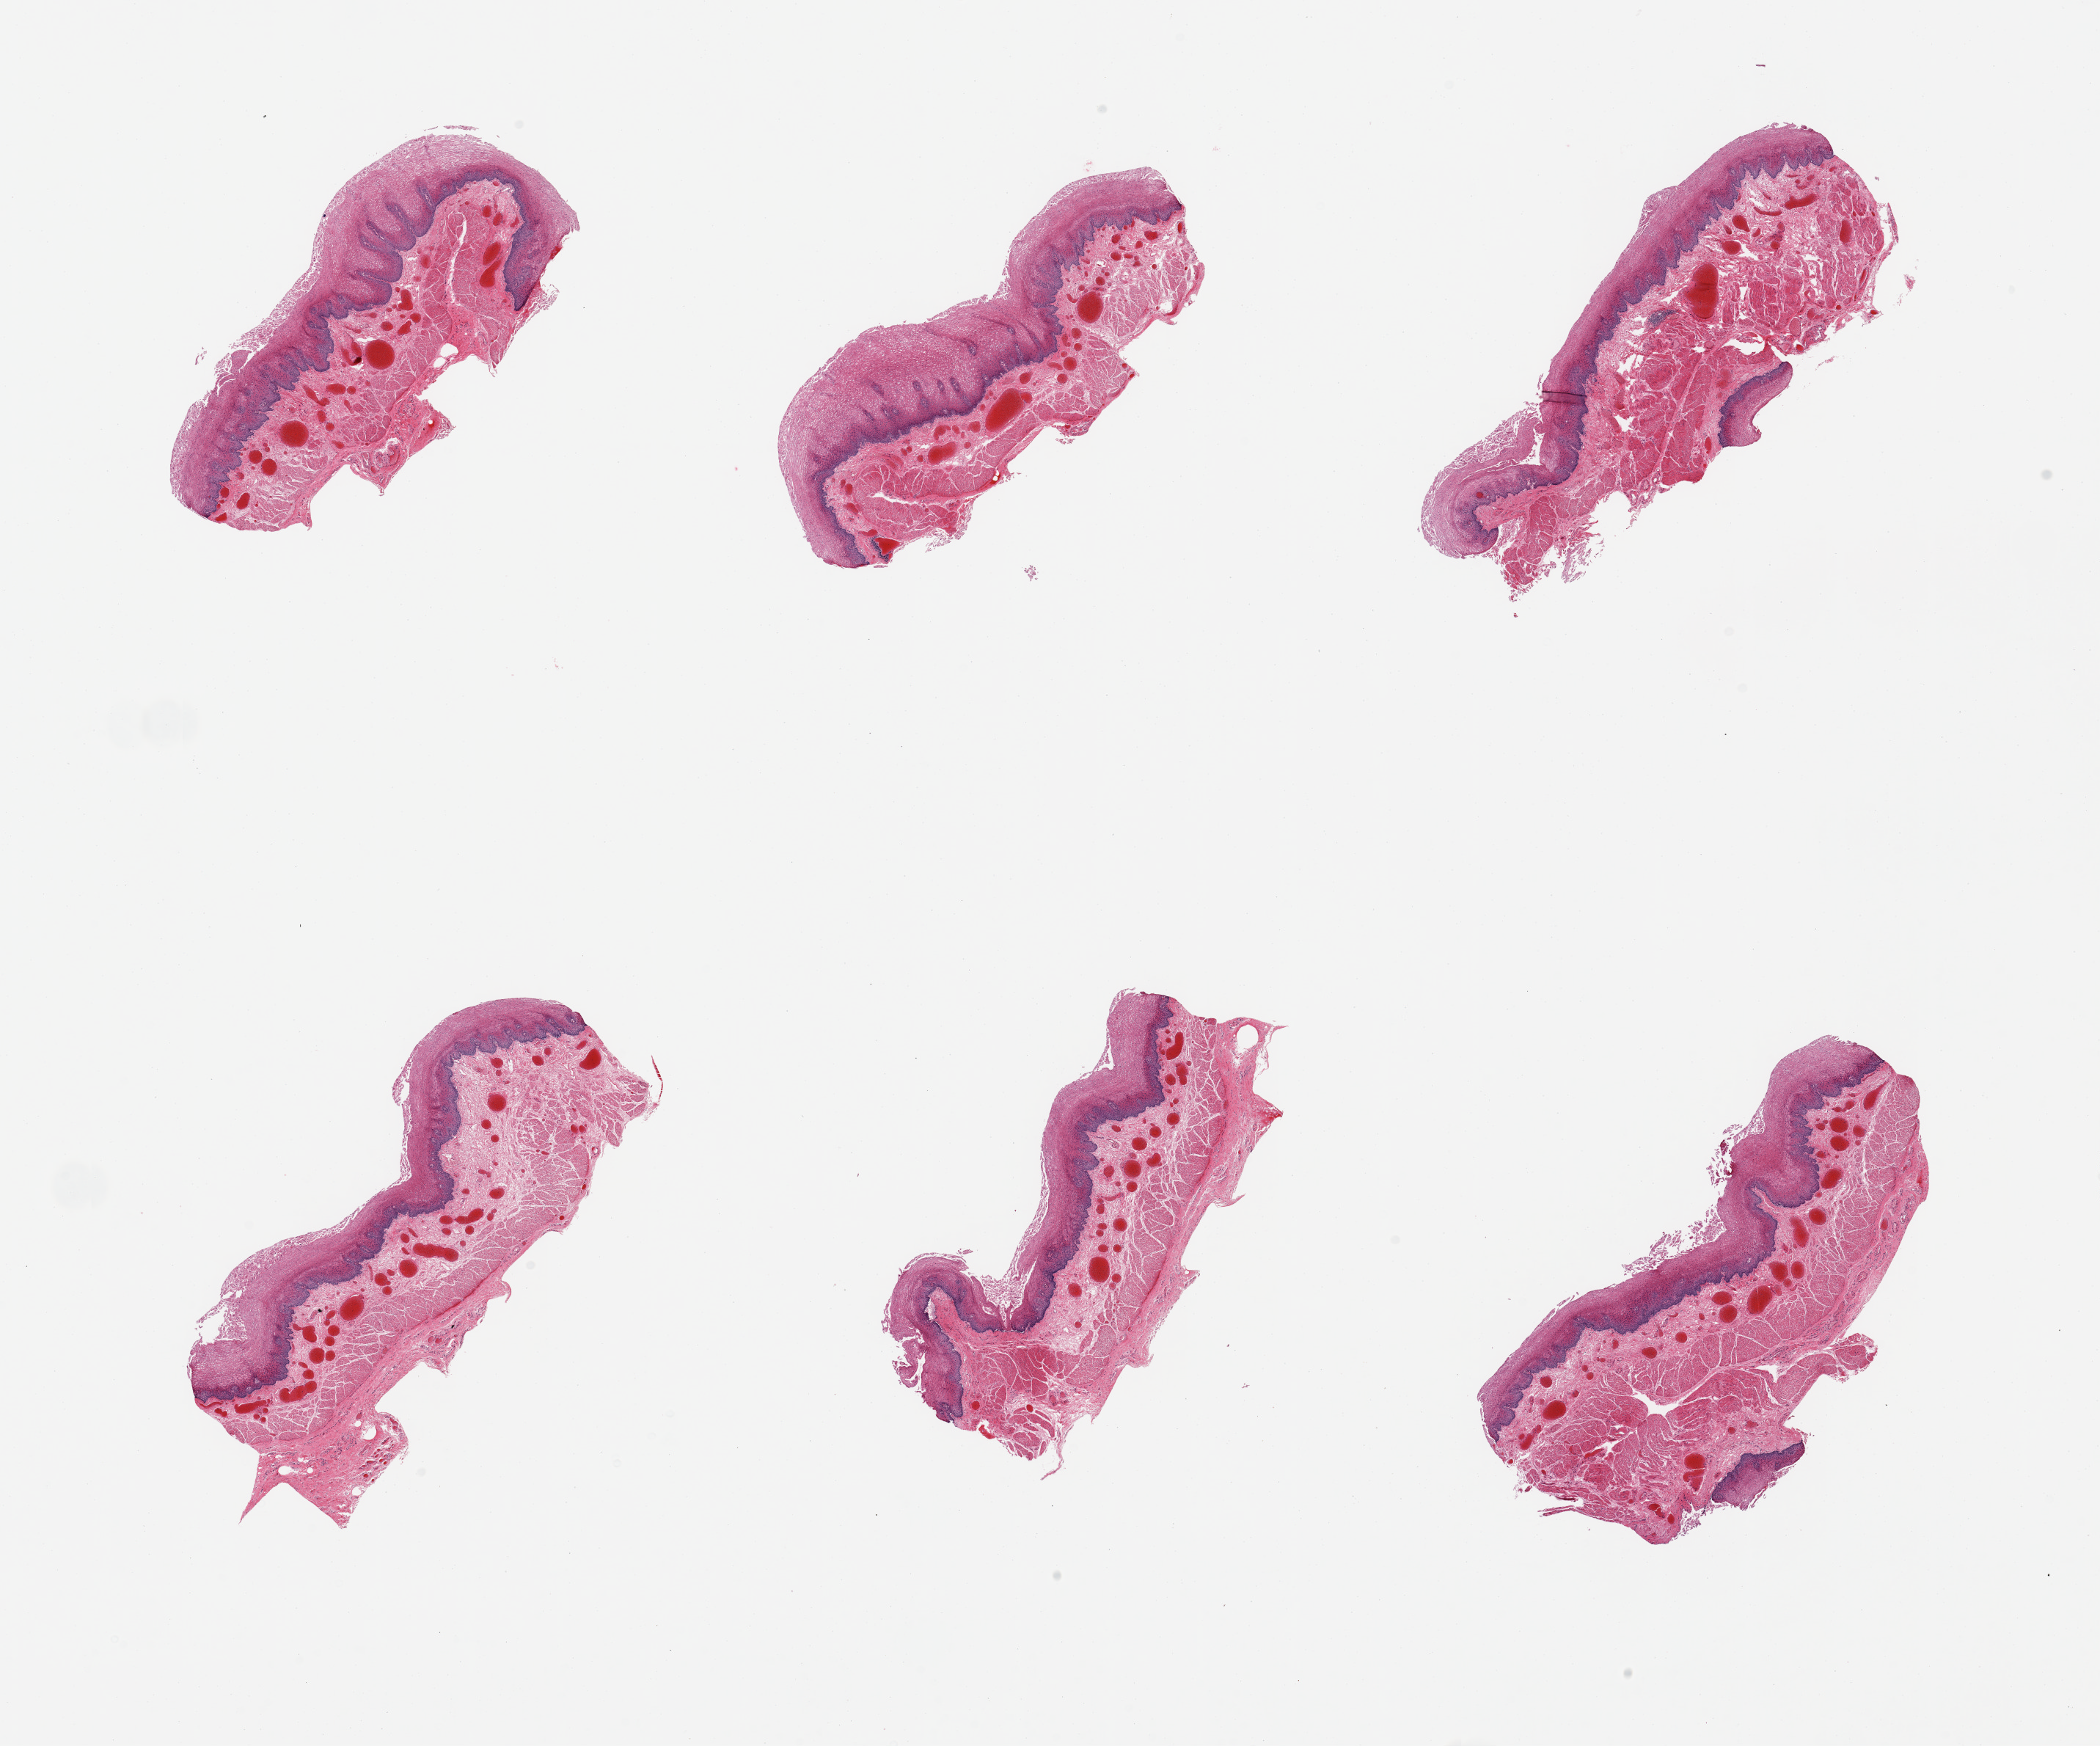
Digitized H&E-stained section, shown as a low-resolution overview of the whole scanned area (about 22.6 x 18.8 mm, from a 20x scan); PAXgene-fixed paraffin-embedded (PFPE) section; sampled site (target tissue): esophageal mucous membrane; donor tissue sample.
Reviewer comment on this tissue sample: 6 pieces; superficially sloughing.